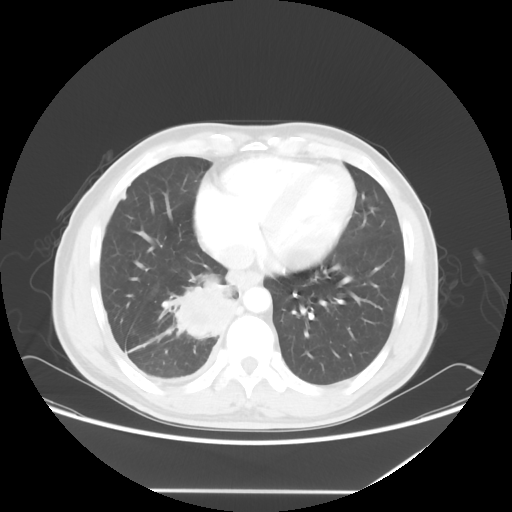
Chest CT, one axial slice; position 20 of 60 along the scan axis; lung window (W 1500 / L -600 HU); 512 × 512 image matrix, field of view 419 × 419 mm. Male patient, age 48 years. From the clinical record (not read from this slice): clinical TNM (as recorded): T3 N3 M1a.
Annotated regions visible in this slice (rectangle marked by the reading radiologist):
- lung tumour (recorded histology: squamous cell carcinoma): bounding box (x1, y1, x2, y2) in pixels: (157, 268, 240, 345)